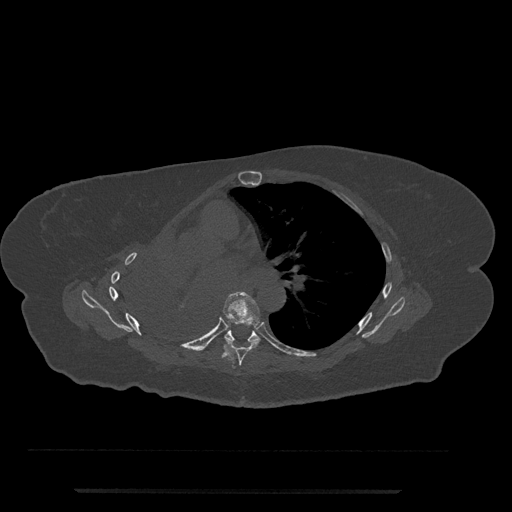
CT including the spine, one axial slice. Position 473 of 797 along the scan axis. 120 kVp. Bone window (W 1800 / L 400 HU). 0.5 mm slice thickness. 512 × 512 image matrix, field of view 440 × 440 mm. Female patient, age 51 years. Case-level facts recorded for this patient, not image findings: primary cancer: neuro.
Structures marked on this image (semi-automatically segmented with operator editing):
- T6 vertebra: bounding box (x1, y1, x2, y2) in pixels: (223, 291, 260, 366)
- T7 vertebra: (224, 329, 260, 342)